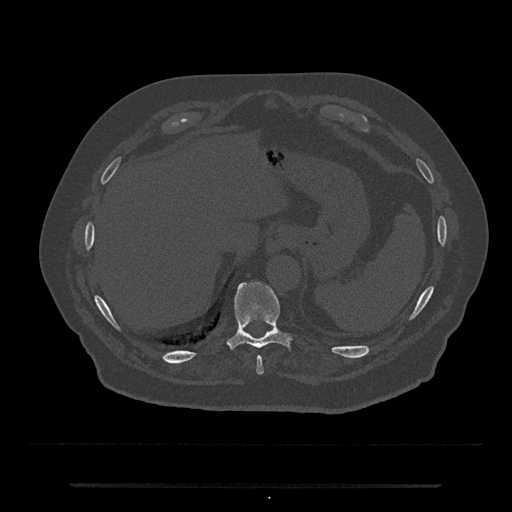
CT including the spine, one axial slice. Slice 708 of 797 in the series (ordered by position). 120 kVp. Bone window (W 1800 / L 400 HU). 0.5 mm slice thickness. 512 × 512 image matrix, field of view 434 × 434 mm. Male patient, age 80 years. From the clinical record (not read from this slice): primary cancer: prostate; vertebrae with lytic lesions (as recorded): L1, T11.
Structures marked on this image (semi-automatically segmented with operator editing):
- T10 vertebra: bounding box (x1, y1, x2, y2) in pixels: (228, 281, 291, 349)
- T9 vertebra: (256, 356, 264, 375)